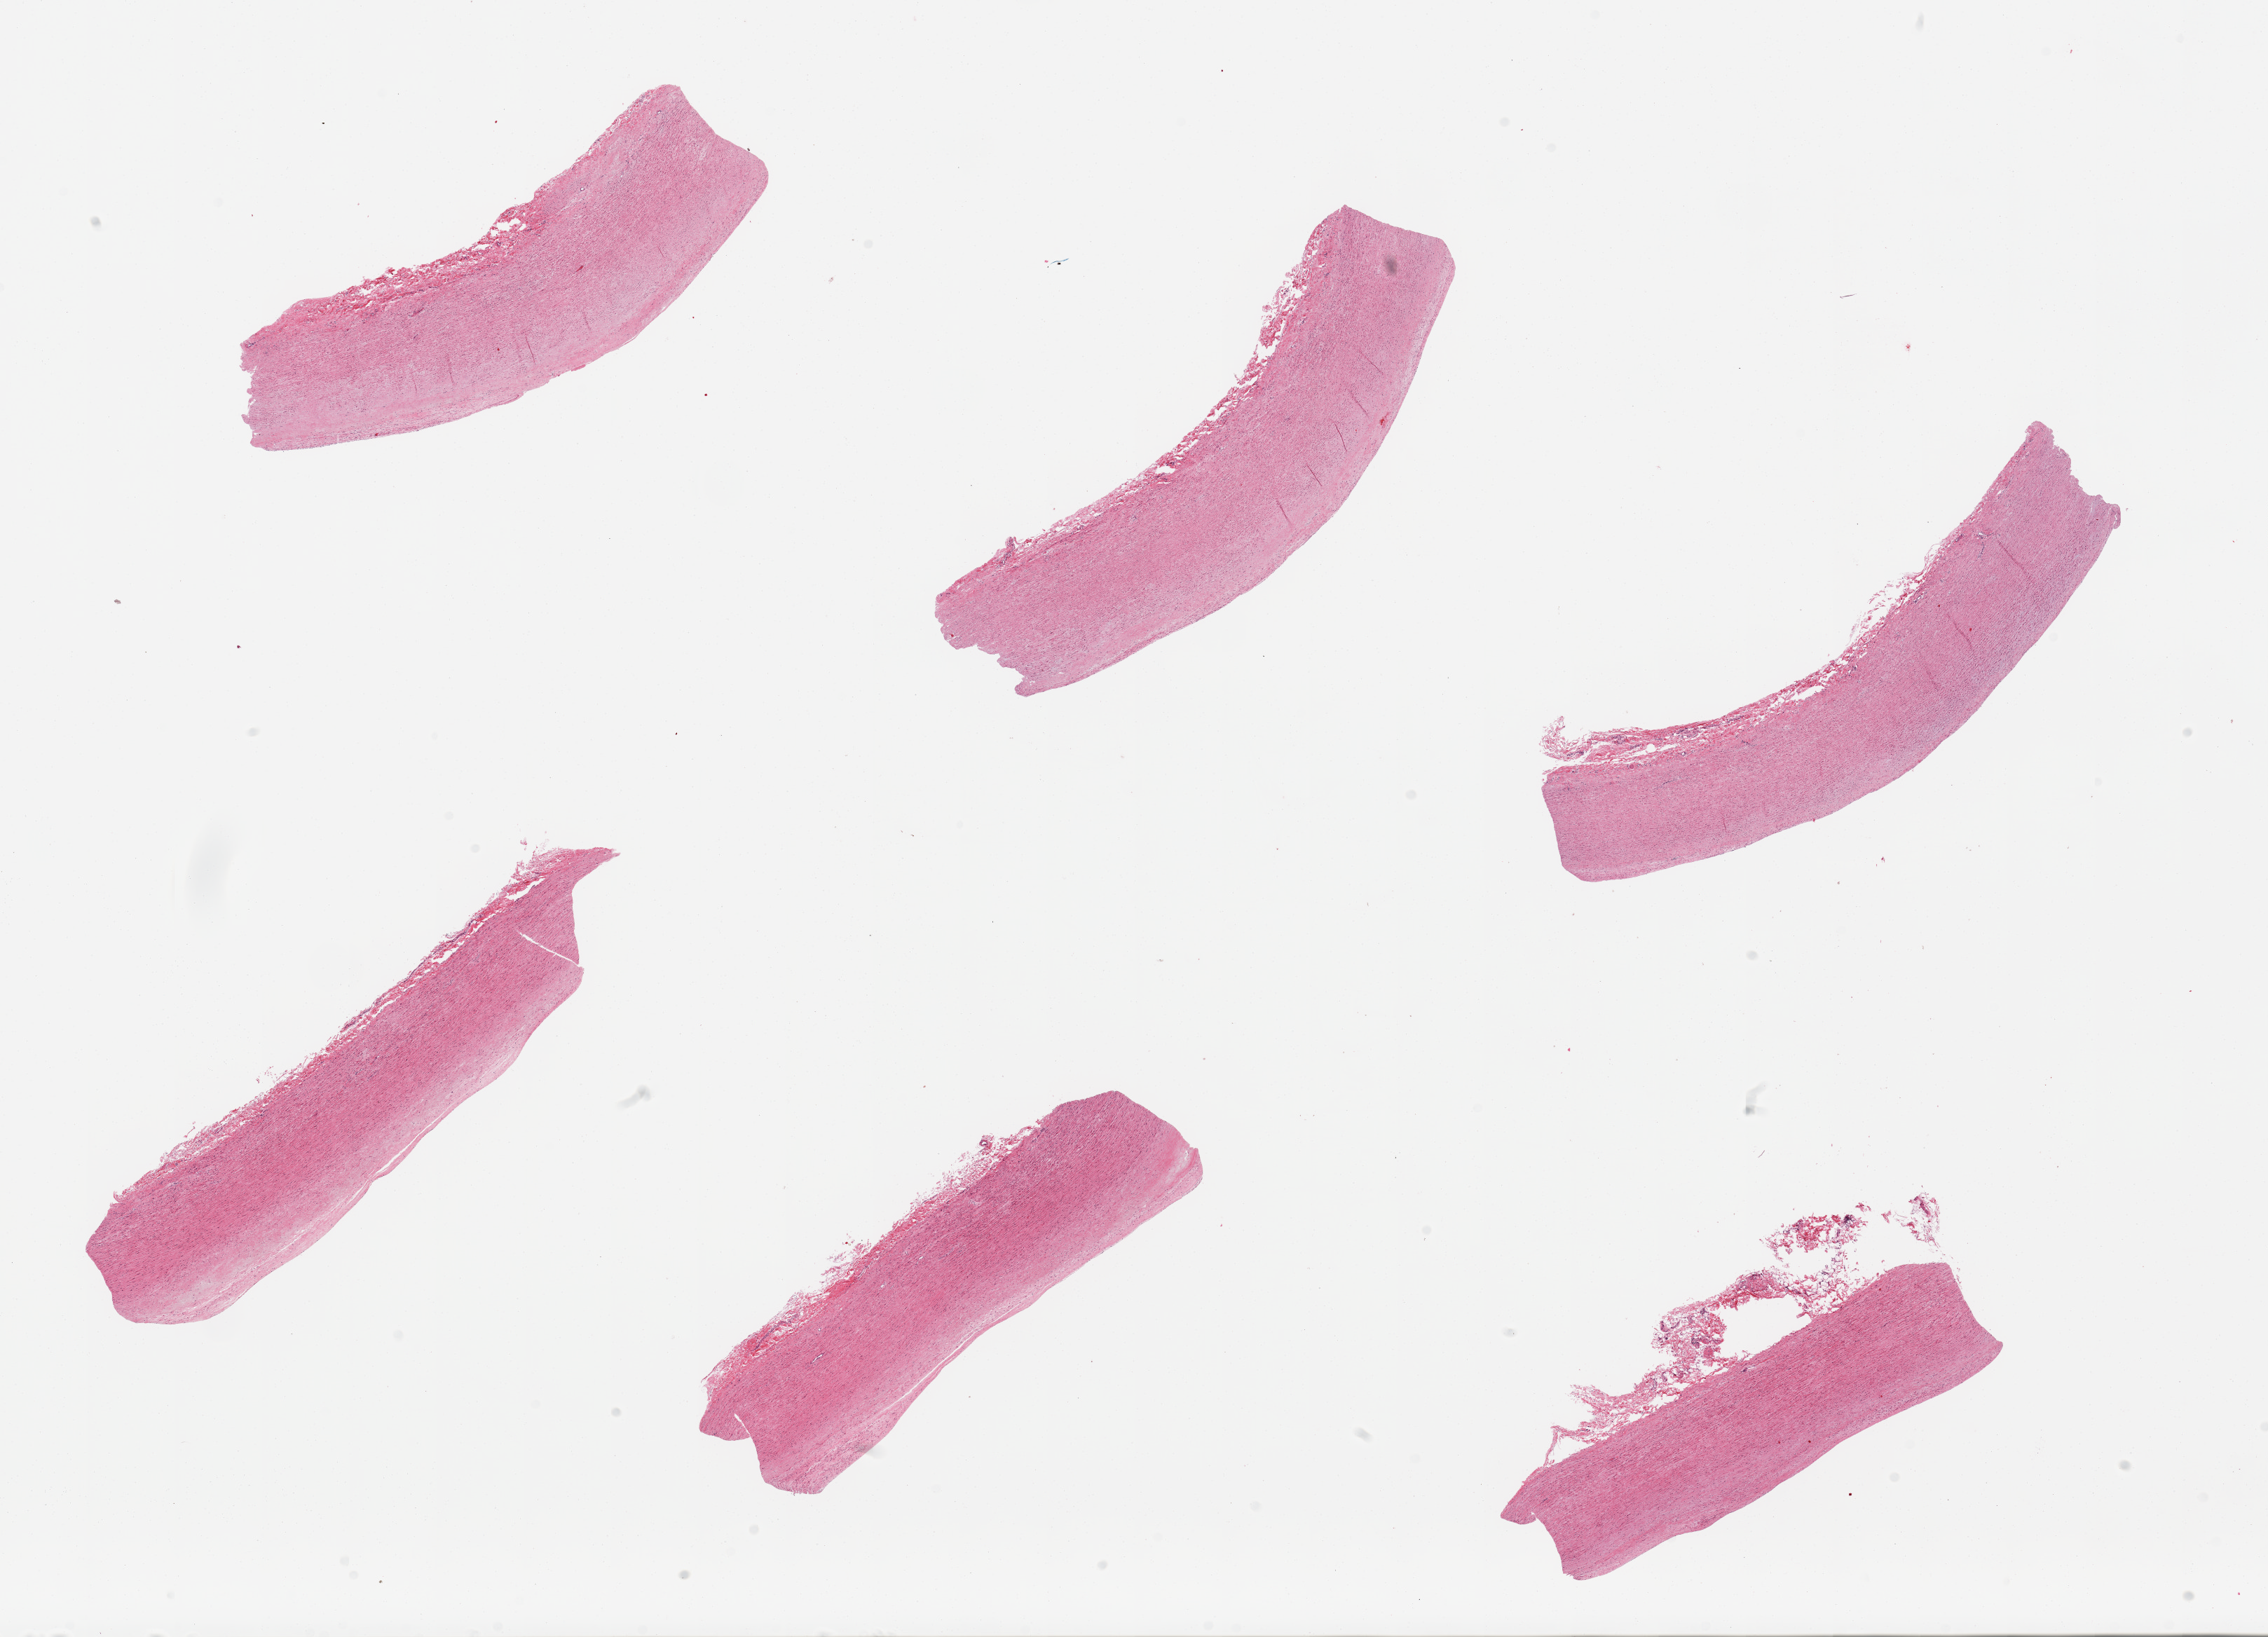
Digitized haematoxylin and eosin-stained section, shown as a low-resolution overview of the whole scanned area (about 25.6 x 18.5 mm). PAXgene-fixed, paraffin-embedded tissue. Target tissue: aorta. Donor tissue sample.
Pathologist's review note for this sample: 6 pieces.